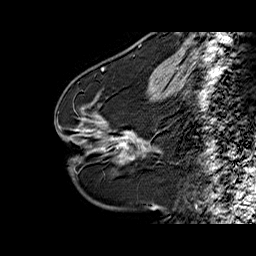
Breast MRI (dynamic contrast-enhanced), one sagittal slice. Slice 25 of 60 in the series (ordered by position). Dynamic contrast-enhanced series, time point 2 of 6 at this slice position (early post-contrast). 1.5 T. TE 6.3 ms, TR 32.5 ms. 4 mm slice thickness. 256 × 256 image matrix, field of view 200 × 200 mm. Female patient. From the clinical record (not read from this slice): setting: breast cancer imaged before/during neoadjuvant chemotherapy; receptor status: HR-positive, HER2-negative.
Structures marked on this image (semi-automatically segmented with operator editing):
- analysis volume of interest (the breast-tissue region the enhancement analysis was run in; not a lesion): box from (x=94, y=103) to (x=161, y=164) px
- tumour enhancement mask (voxels above the 100 % enhancement threshold inside the analysis volume of interest): (x=120, y=142)–(x=126, y=145)